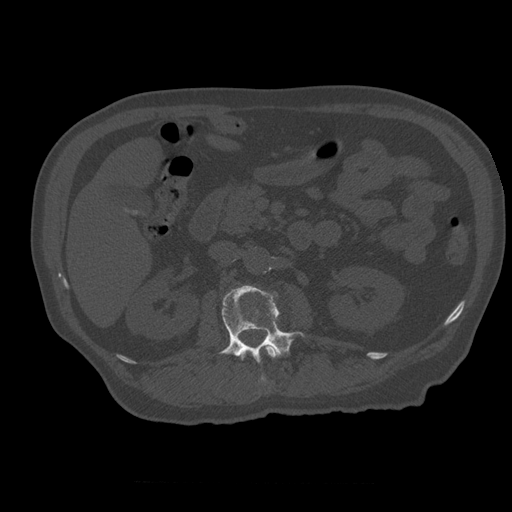
CT including the spine, one axial slice. Slice 217 of 399 in the series (ordered by position). Reconstruction kernel STANDARD. 120 kVp. Bone window (W 1800 / L 400 HU). 1.25 mm slice thickness. 512 × 512 image matrix, field of view 407 × 407 mm. Patient age 73 years. From the clinical record (not read from this slice): primary cancer: prostate; vertebrae with lytic lesions (as recorded): L2.
Structures marked on this image (semi-automatic segmentation, software-assisted and operator-edited):
- L1 vertebra: bounding box [x1, y1, x2, y2] px = [241, 345, 278, 360]
- L2 vertebra: [219, 286, 304, 386]